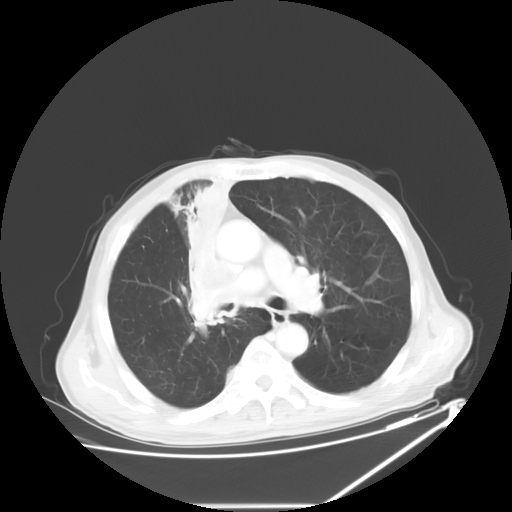
Chest CT, one axial slice. Position 38 of 60 along the scan axis. Reconstruction kernel STANDARD. 120 kVp. Lung window (W 1500 / L -600 HU). 512 × 512 image matrix. Male patient, age 73 years. Case-level facts recorded for this patient, not image findings: clinical TNM (as recorded): T2a N1 M0.
Outlined on this slice (rectangle marked by the reading radiologist):
- lung tumour (recorded histology: squamous cell carcinoma): bounding box [x1, y1, x2, y2] px = [171, 175, 236, 336]